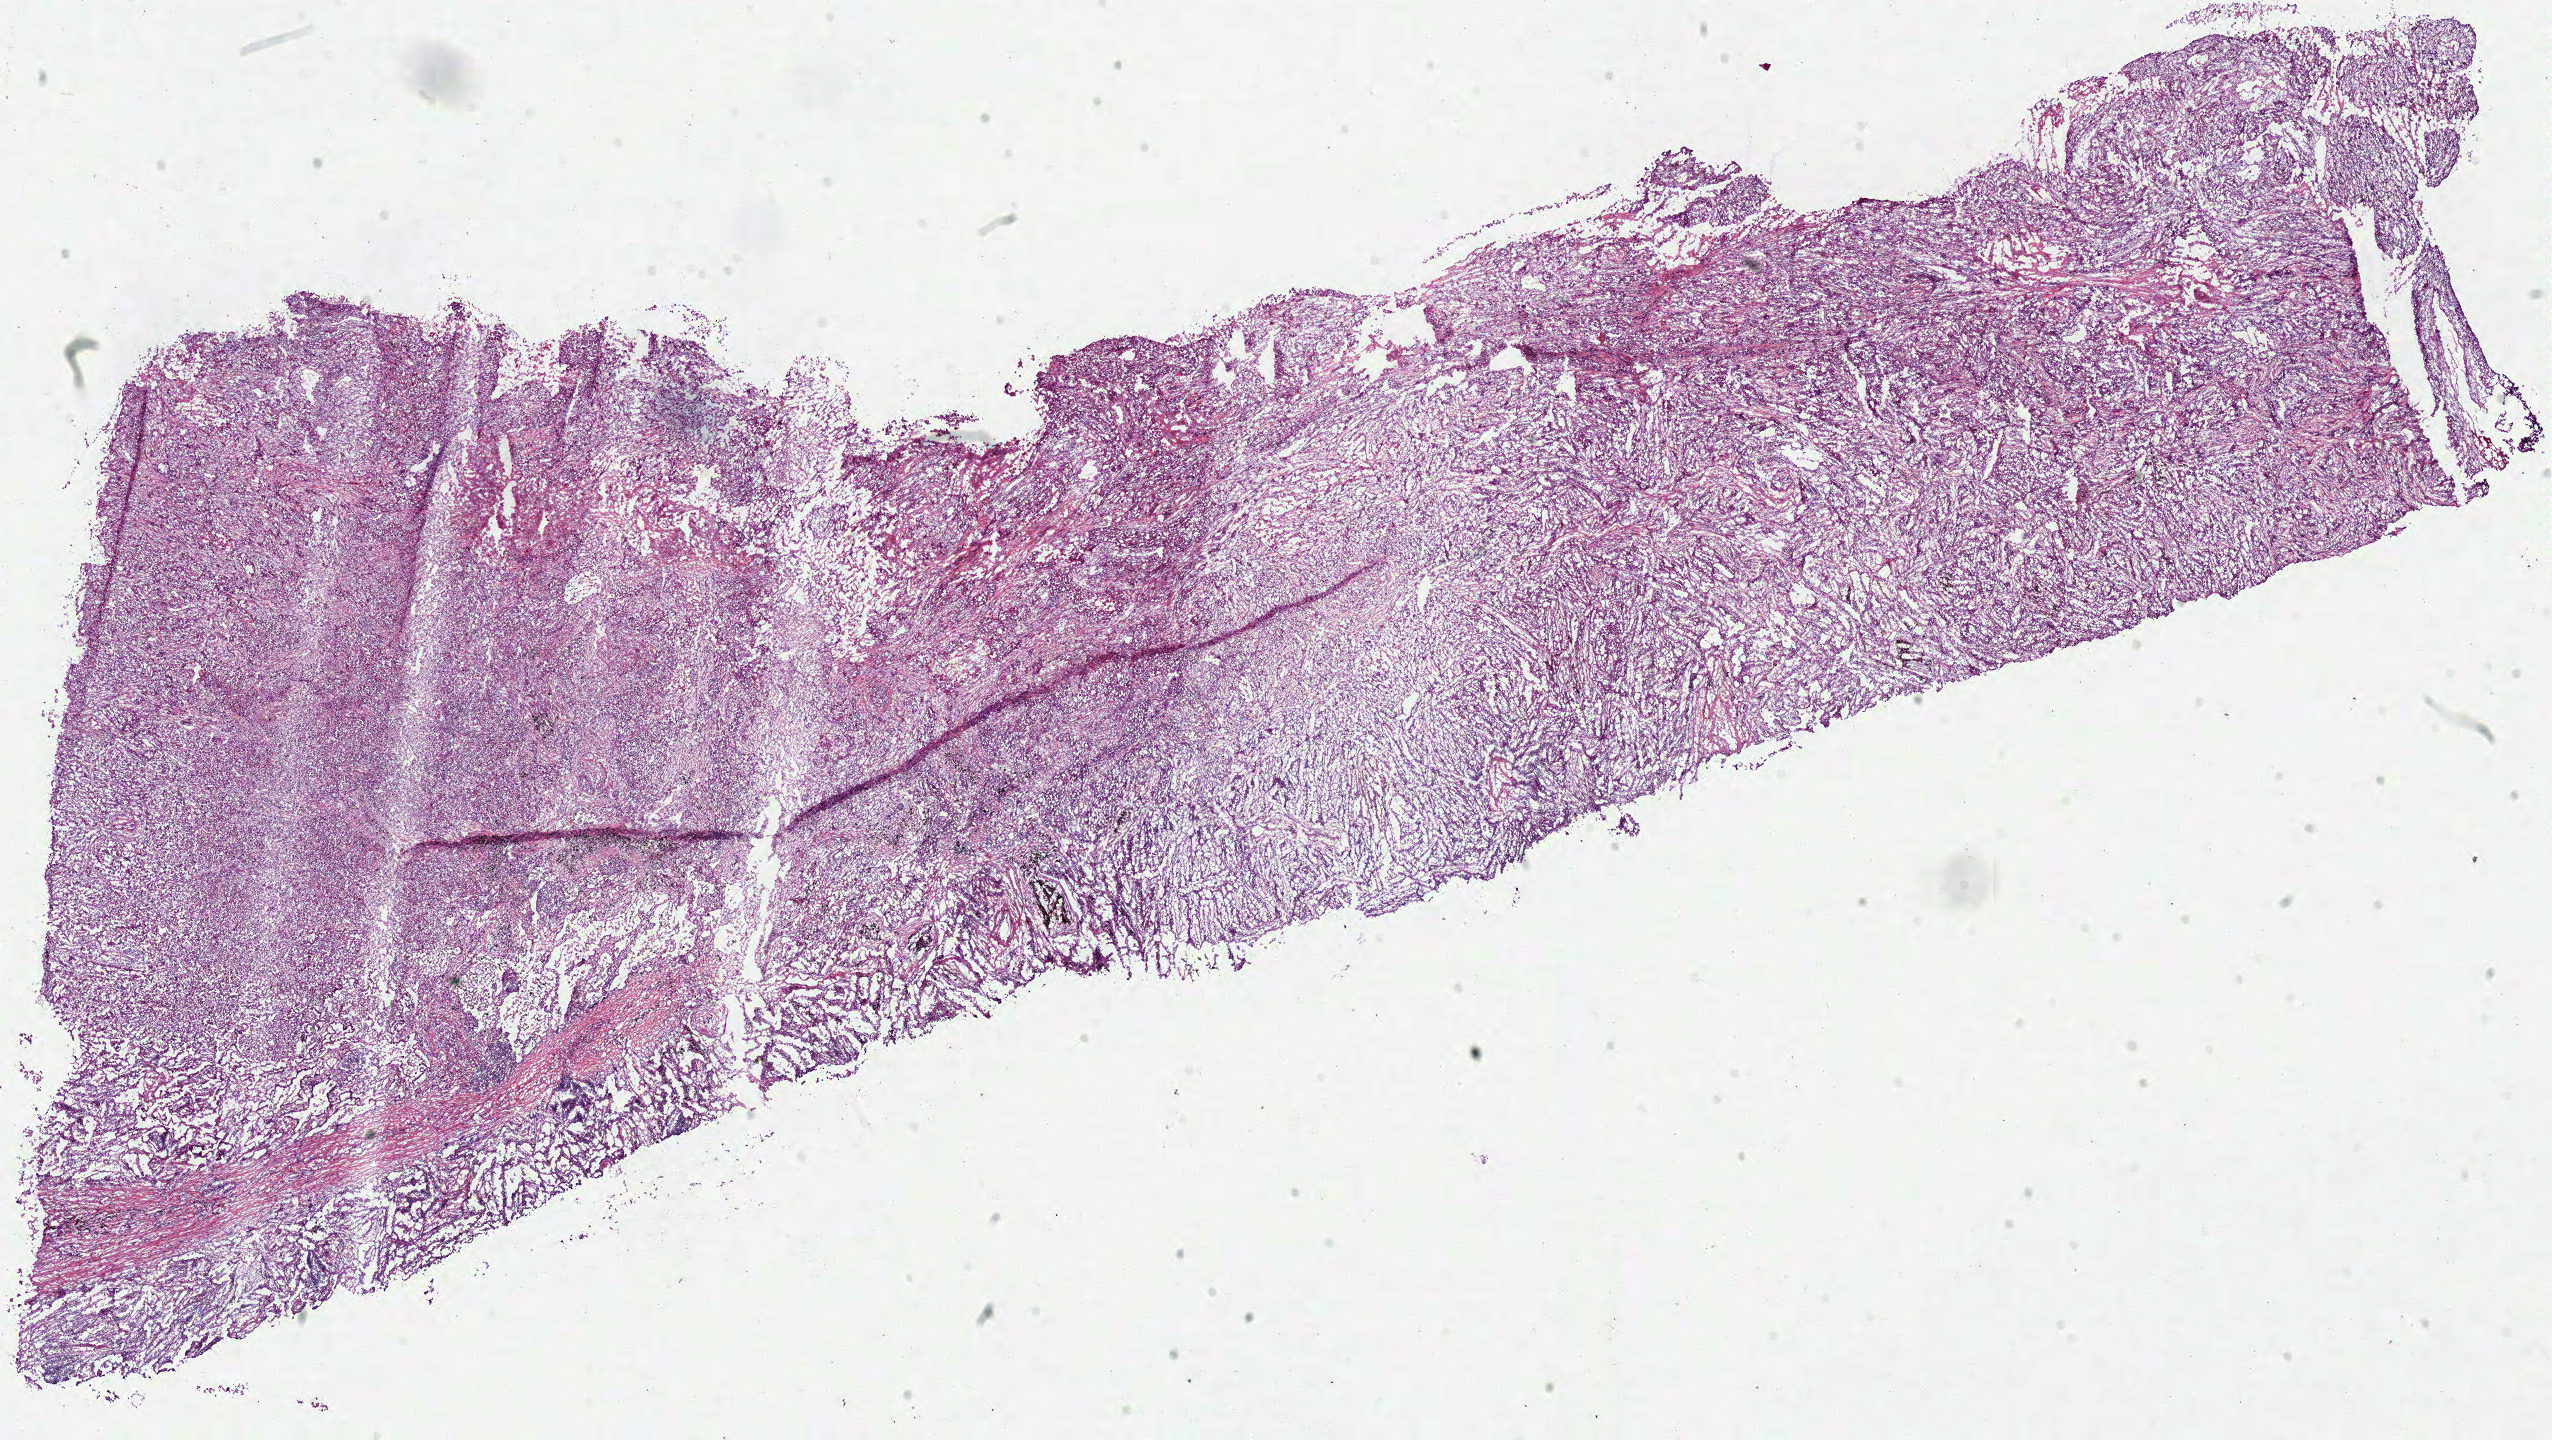
H&E whole-slide image, whole scanned area (about 20.1 x 11.3 mm) shown as a low-resolution overview. Frozen section from the bottom of the tissue portion. Sample: primary tumour, lung. Male patient; age at initial diagnosis 47 years. Slide review estimates, as recorded: tumour cells 72%, tumour nuclei 75%, normal cells 10%, stromal cells 10%, necrosis 8%.
* histologic diagnosis: Squamous cell carcinoma, NOS (upper lobe, lung)
* AJCC pathologic stage: IIIA (6th edition)